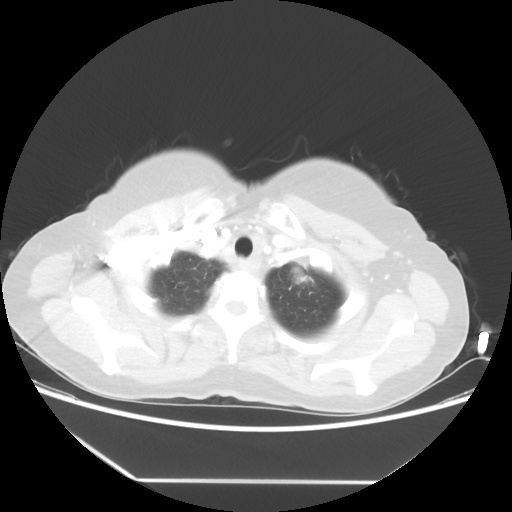
Chest CT, one axial slice. Position 47 of 52 along the scan axis. Reconstruction kernel STANDARD. Lung window (W 1500 / L -600 HU). 5 mm slice thickness. 512 × 512 image matrix. Patient: female, 50 years. From the clinical record (not read from this slice): clinical TNM (as recorded): T2 N3 M0.
Annotated regions visible in this slice (bounding box drawn by a radiologist):
- lung tumour (recorded histology: adenocarcinoma): bounding box <281,256,327,294> (left, top, right, bottom; pixels)